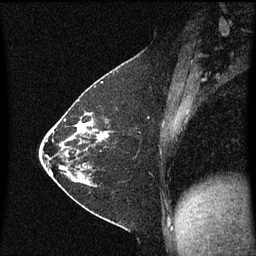
Breast MRI (dynamic contrast-enhanced), one sagittal slice. Slice 28 of 60 in the series (ordered by position). Dynamic contrast-enhanced series, image 2 of 3 at this slice position (ordered by acquisition). 1.5 T. TE 4.2 ms, TR 8.4 ms. 2 mm slice thickness. 256 × 256 image matrix, field of view 200 × 200 mm. Patient: female, 36 years. Case-level facts recorded for this patient, not image findings: setting: breast cancer imaged before/during neoadjuvant chemotherapy; receptor status: HR-positive, HER2-negative.
Annotated regions visible in this slice (semi-automatic segmentation, software-assisted and operator-edited):
- analysis volume of interest (the breast-tissue region the enhancement analysis was run in; not a lesion): bounding box [x1, y1, x2, y2] px = [72, 116, 109, 187]
- tumour enhancement mask (voxels above the 70 % enhancement threshold inside the analysis volume of interest): [72, 116, 109, 177]